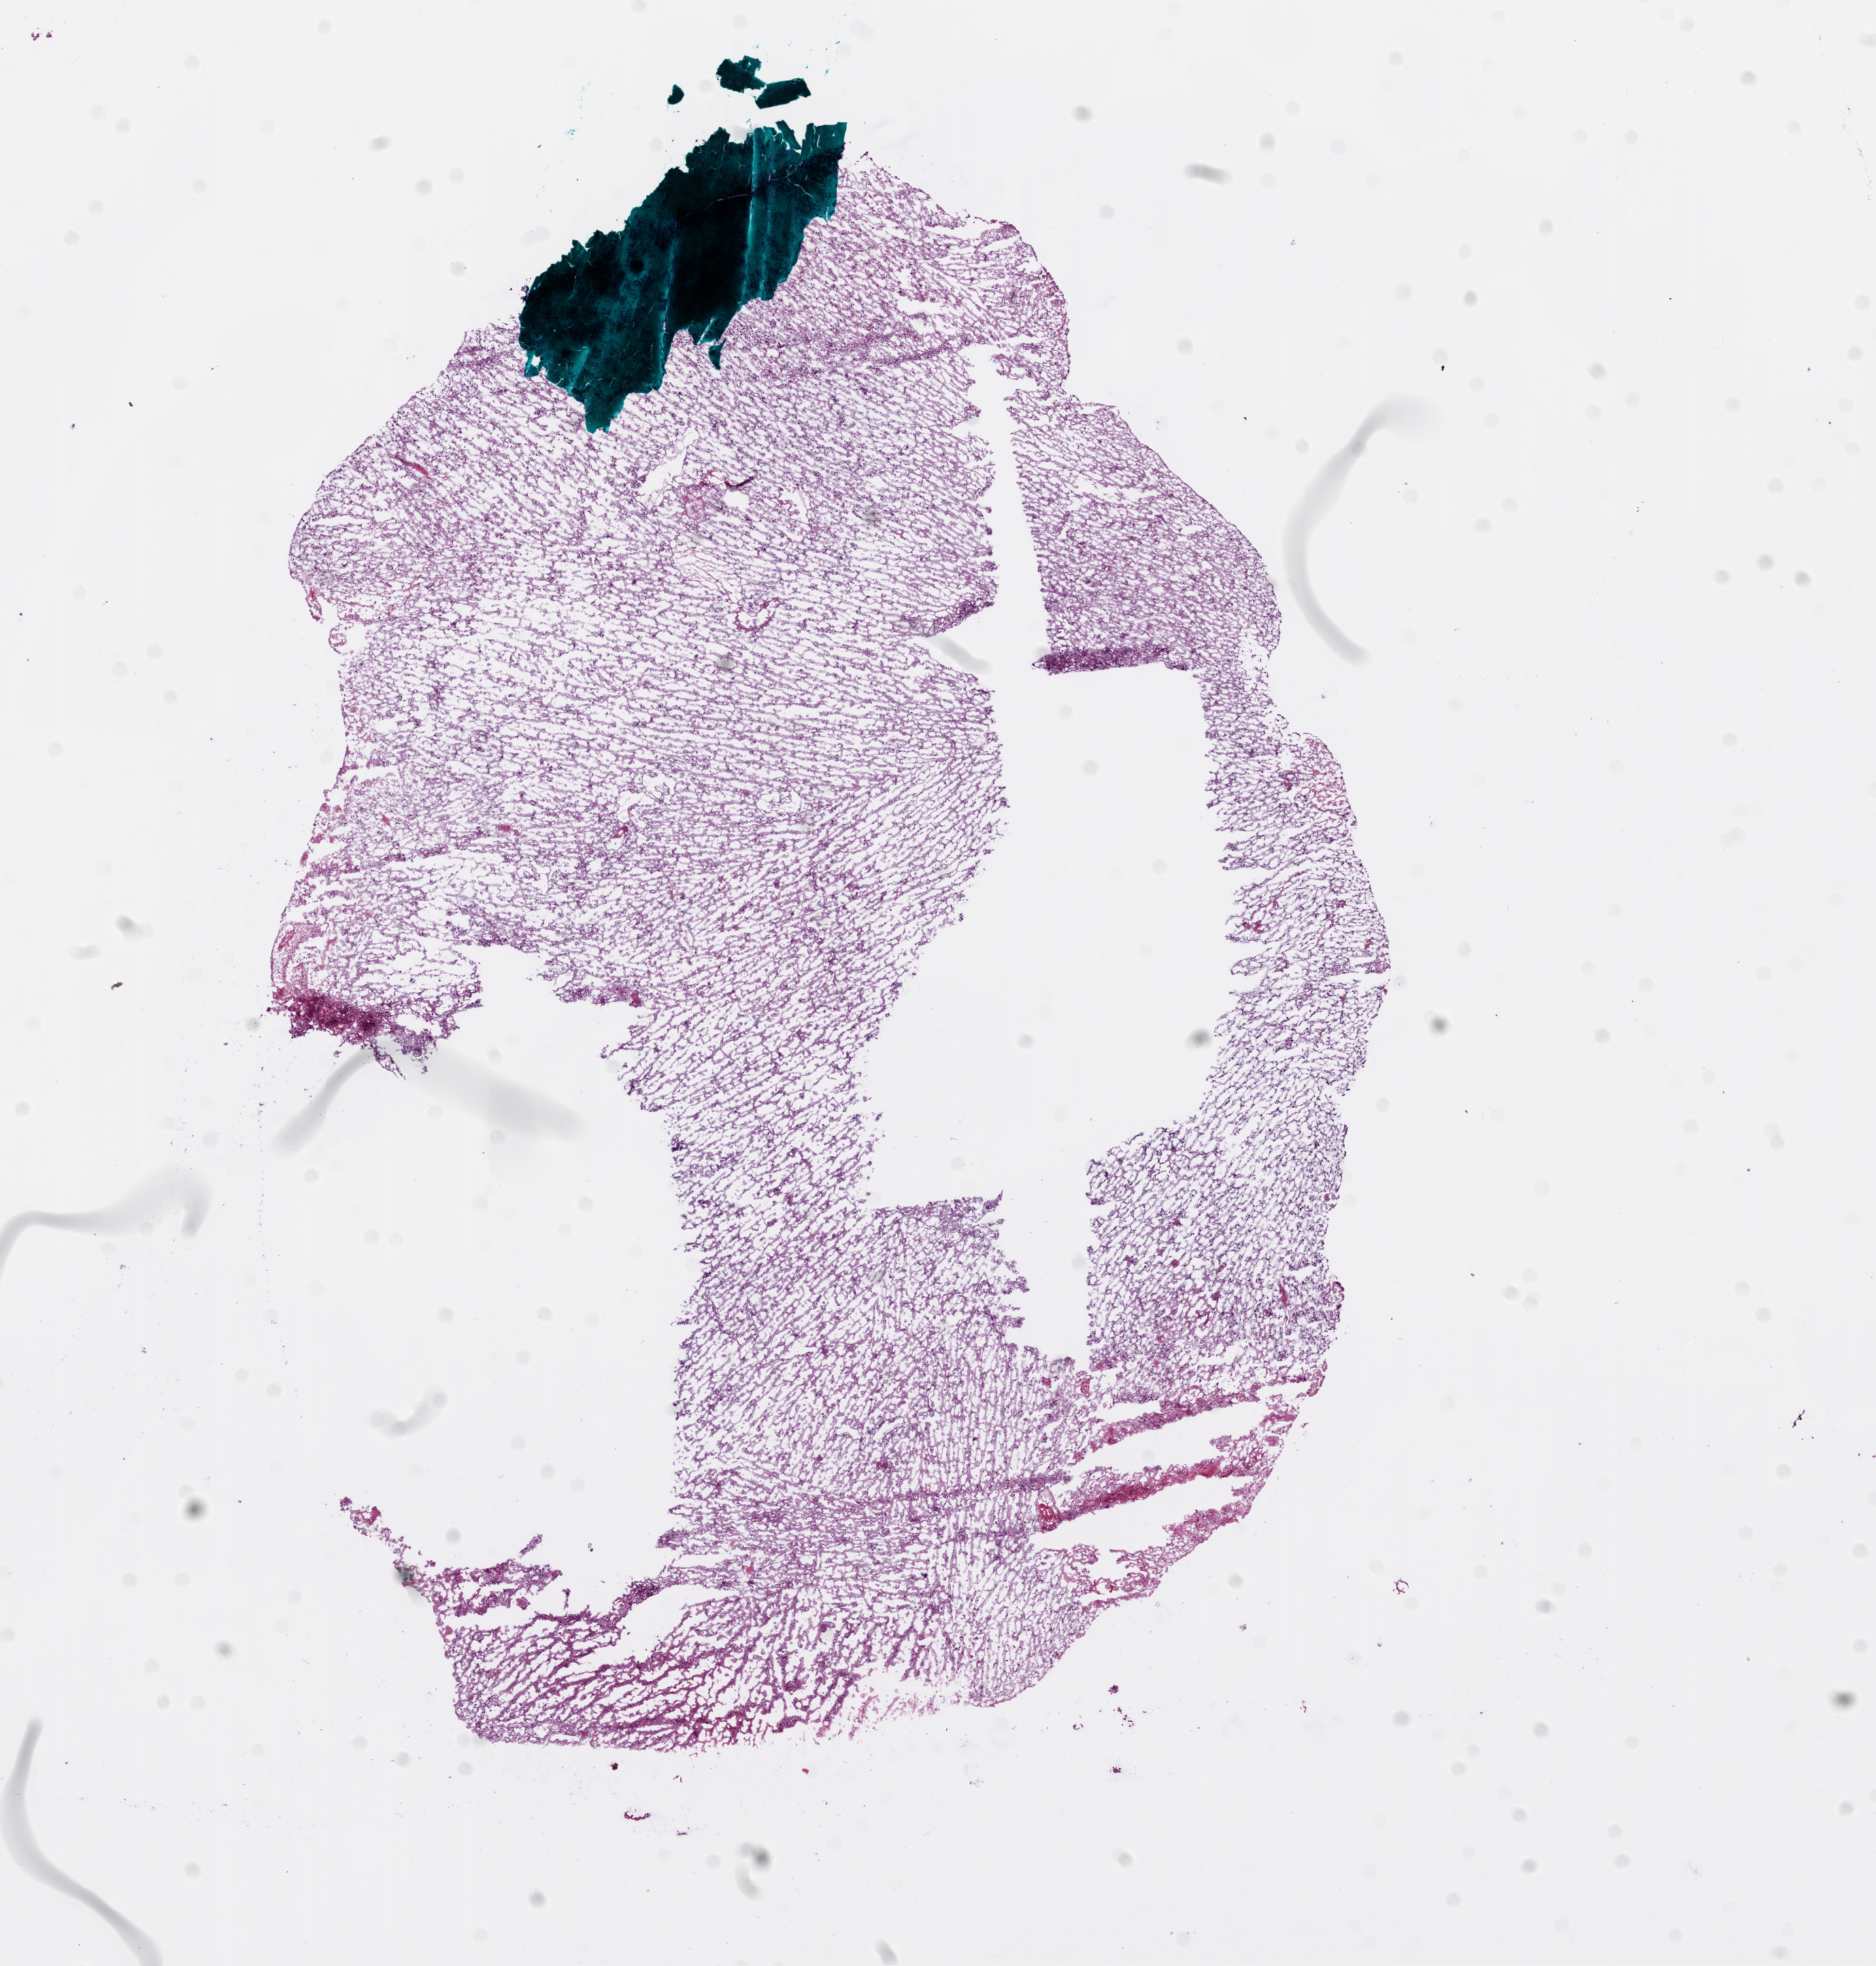
H&E-stained whole-slide image — low-resolution overview of the scanned area, about 11.1 x 11.7 mm (from a 20x scan). Frozen section from the bottom of the tissue portion. Sample: primary tumour, brain. Patient: male, age at initial diagnosis 55 years. Pathologist review of this section (percent, as recorded): tumour cells 75%, tumour nuclei 80%, normal cells 10%, stromal cells 15%, necrosis 0%.
Histologic diagnosis: Glioblastoma.